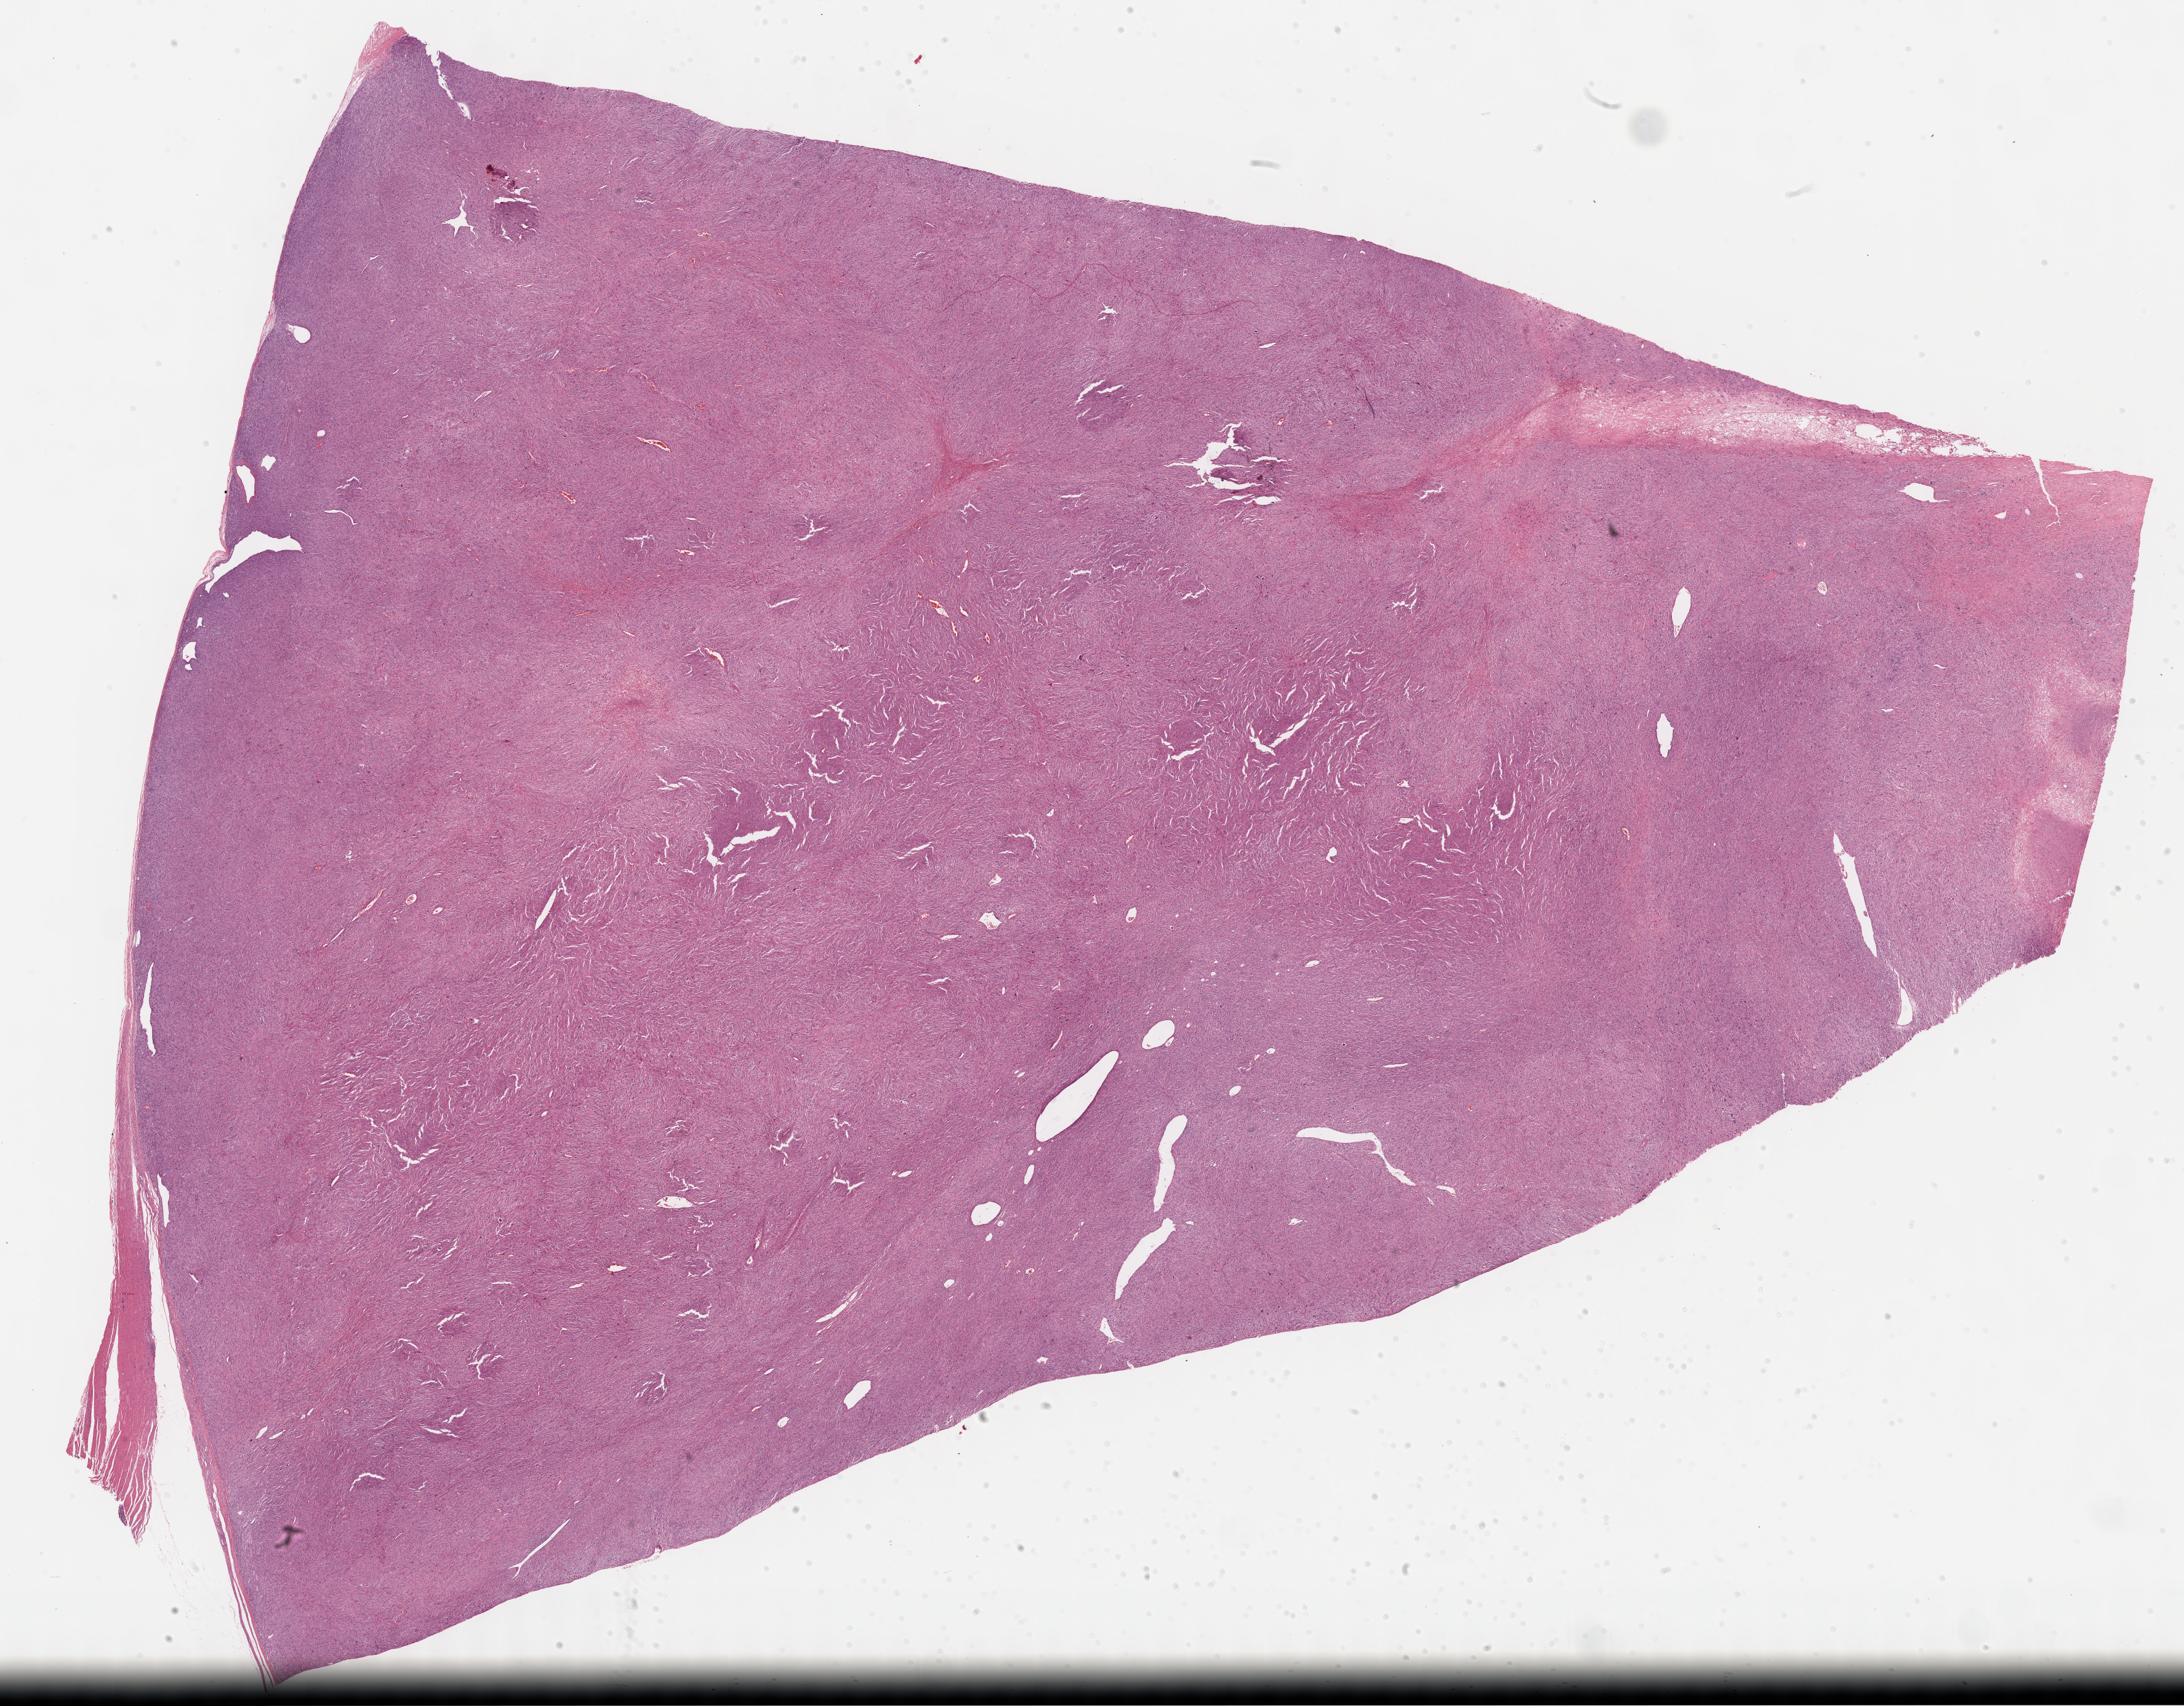
Digitized Hematoxylin and eosin (H&E) stained tissue section (whole slide) — shown as a low-resolution overview of the whole scanned area (about 28.7 x 22.4 mm); formalin-fixed paraffin-embedded (FFPE) diagnostic section; primary tumour sample from the connective, subcutaneous and other soft tissues. Patient: female, age at initial diagnosis 62 years.
Diagnosis: Malignant fibrous histiocytoma (connective, subcutaneous and other soft tissues of lower limb and hip).